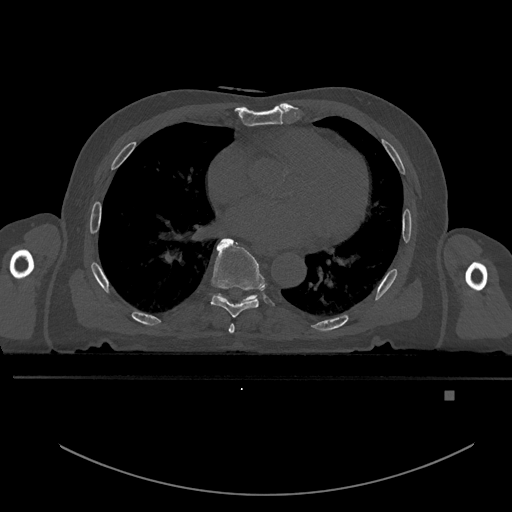
CT including the spine, one axial slice. Position 246 of 969 along the scan axis. Bone window (W 1800 / L 400 HU). 0.5 mm slice thickness. 512 × 512 image matrix, field of view 456 × 456 mm. Male patient, age 82 years. Case-level facts recorded for this patient, not image findings: primary cancer: prostate; vertebrae with lytic lesions (as recorded): T11, T9, T8, T2.
Outlined on this slice (semi-automatically segmented with operator editing):
- T6 vertebra: box from (x=229, y=324) to (x=235, y=333) px
- T7 vertebra: (x=211, y=238)–(x=265, y=318)
- T8 vertebra: (x=214, y=293)–(x=258, y=304)